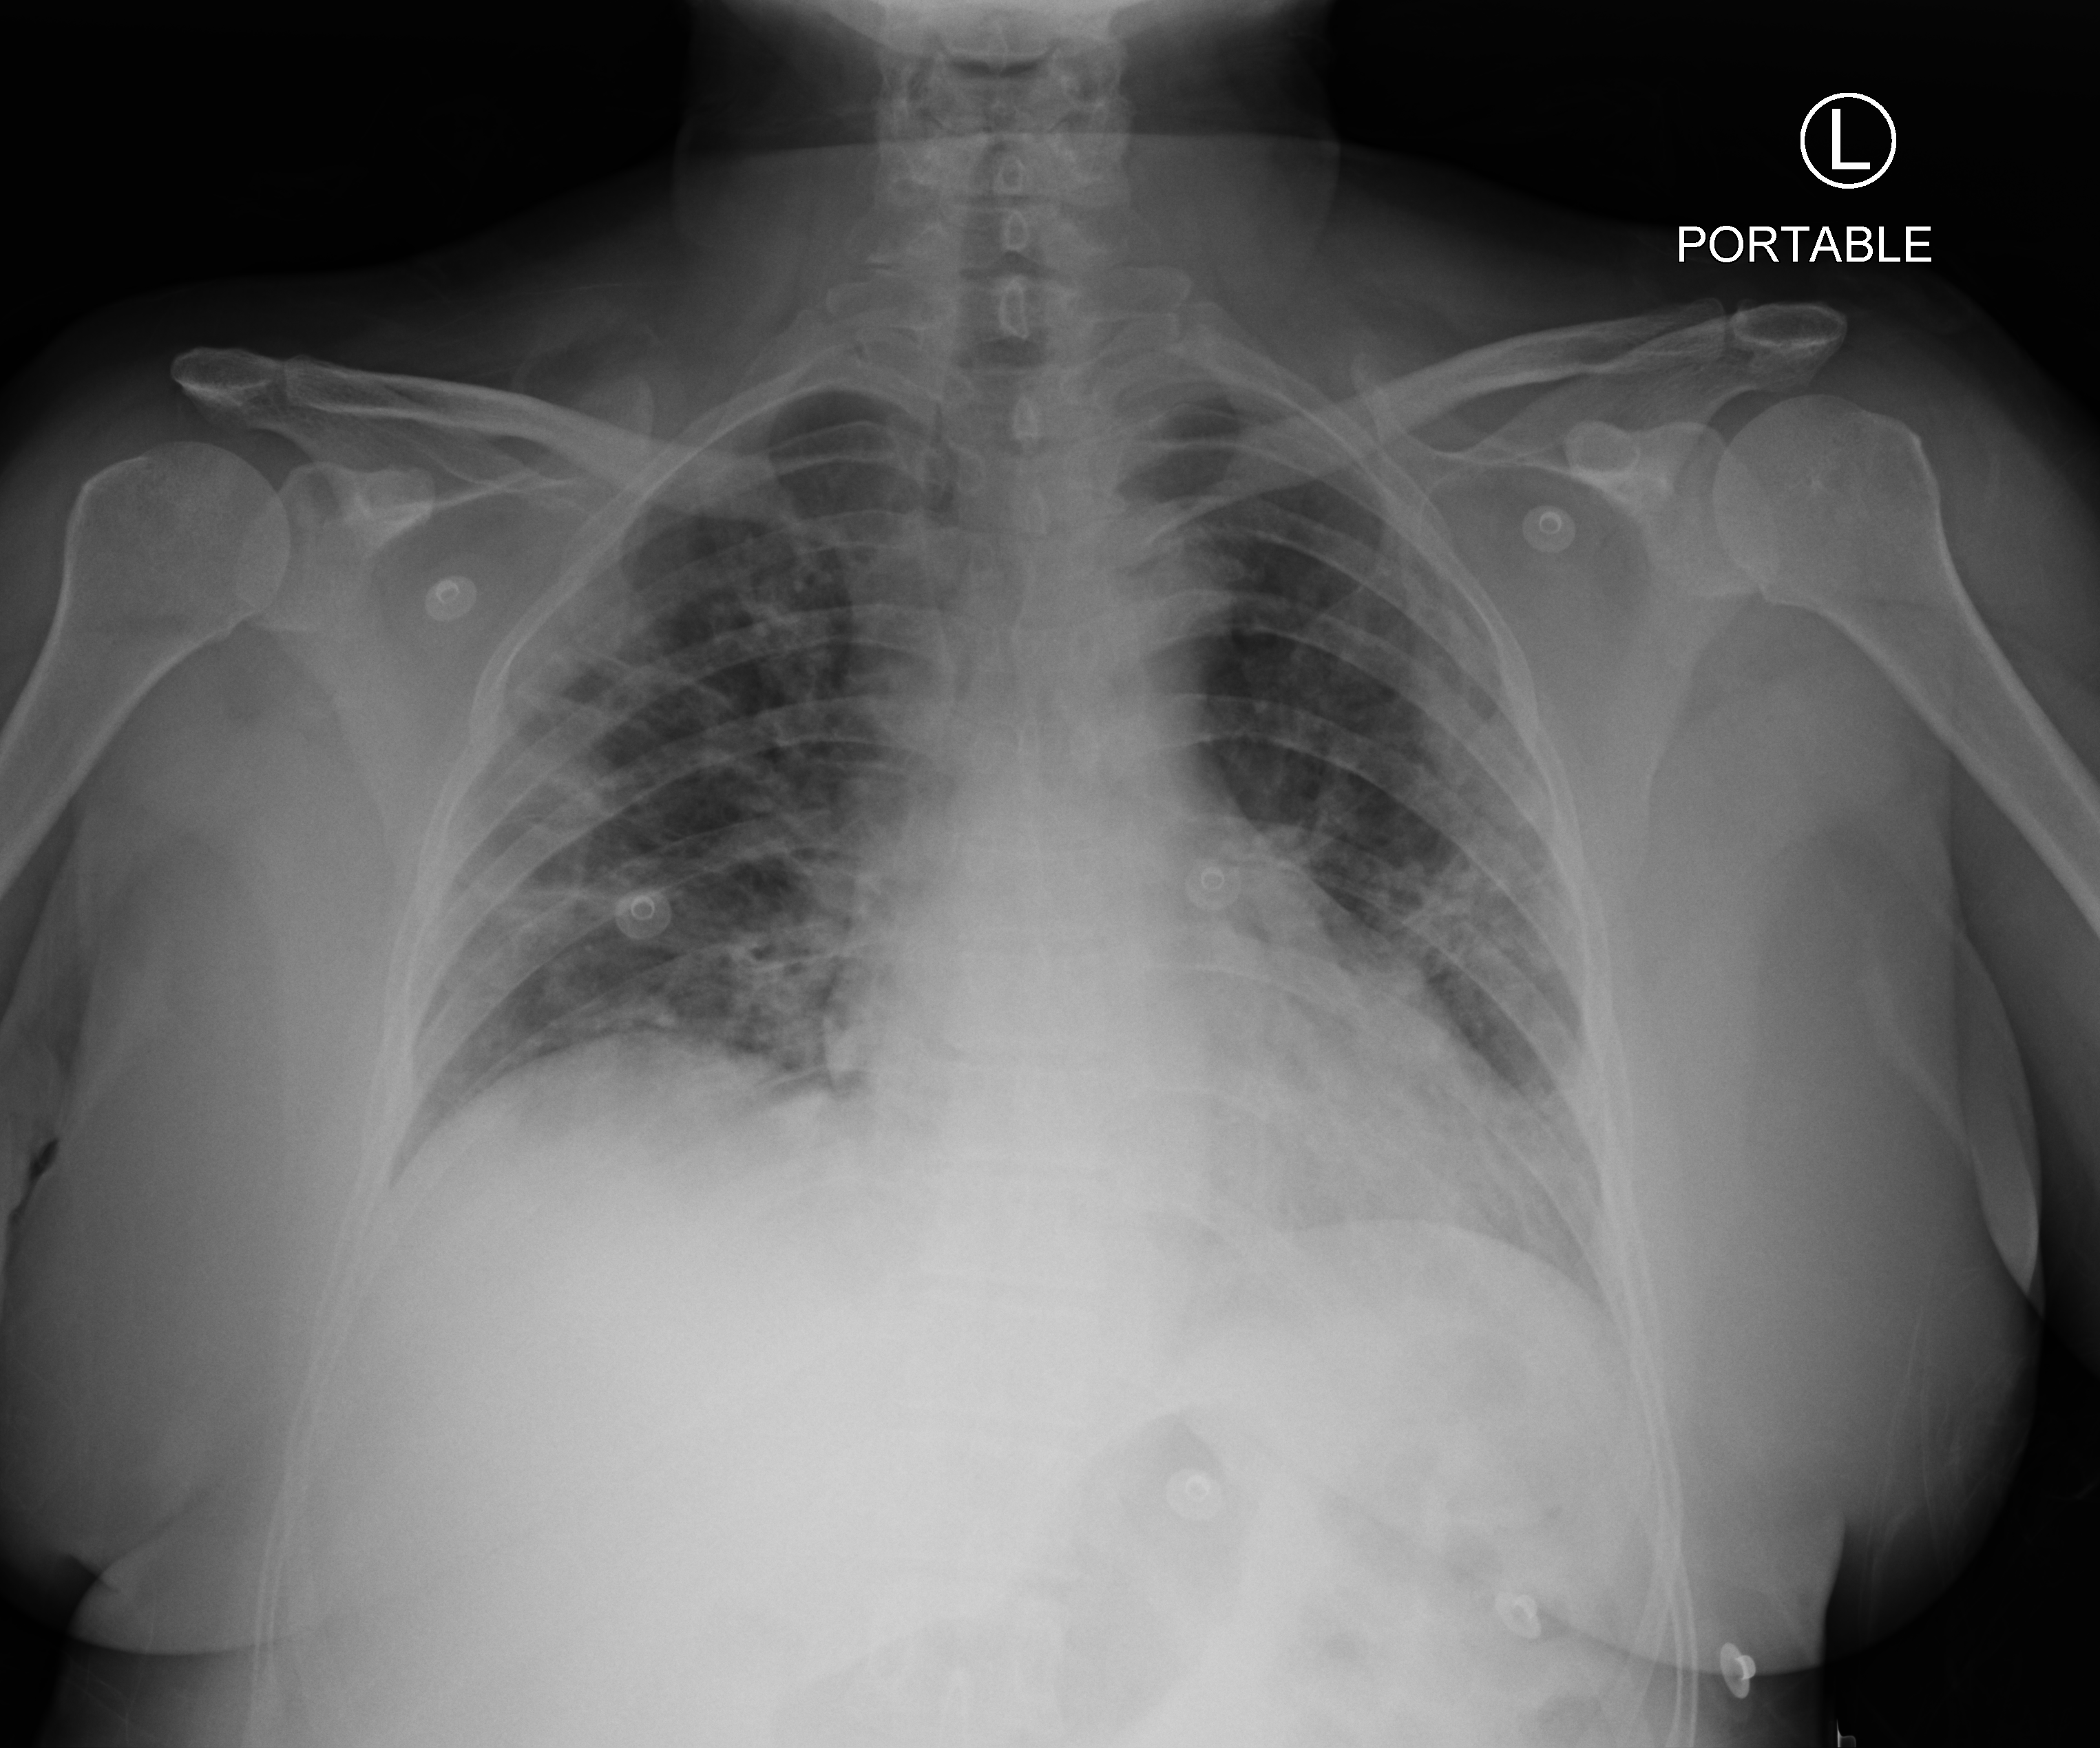
Portable chest radiograph. Female patient hospitalised with COVID-19, age 60–74 years.
From the hospital-stay record, not from the radiograph (when in the stay this image was taken is not recorded):
- length of hospital stay: 5 days